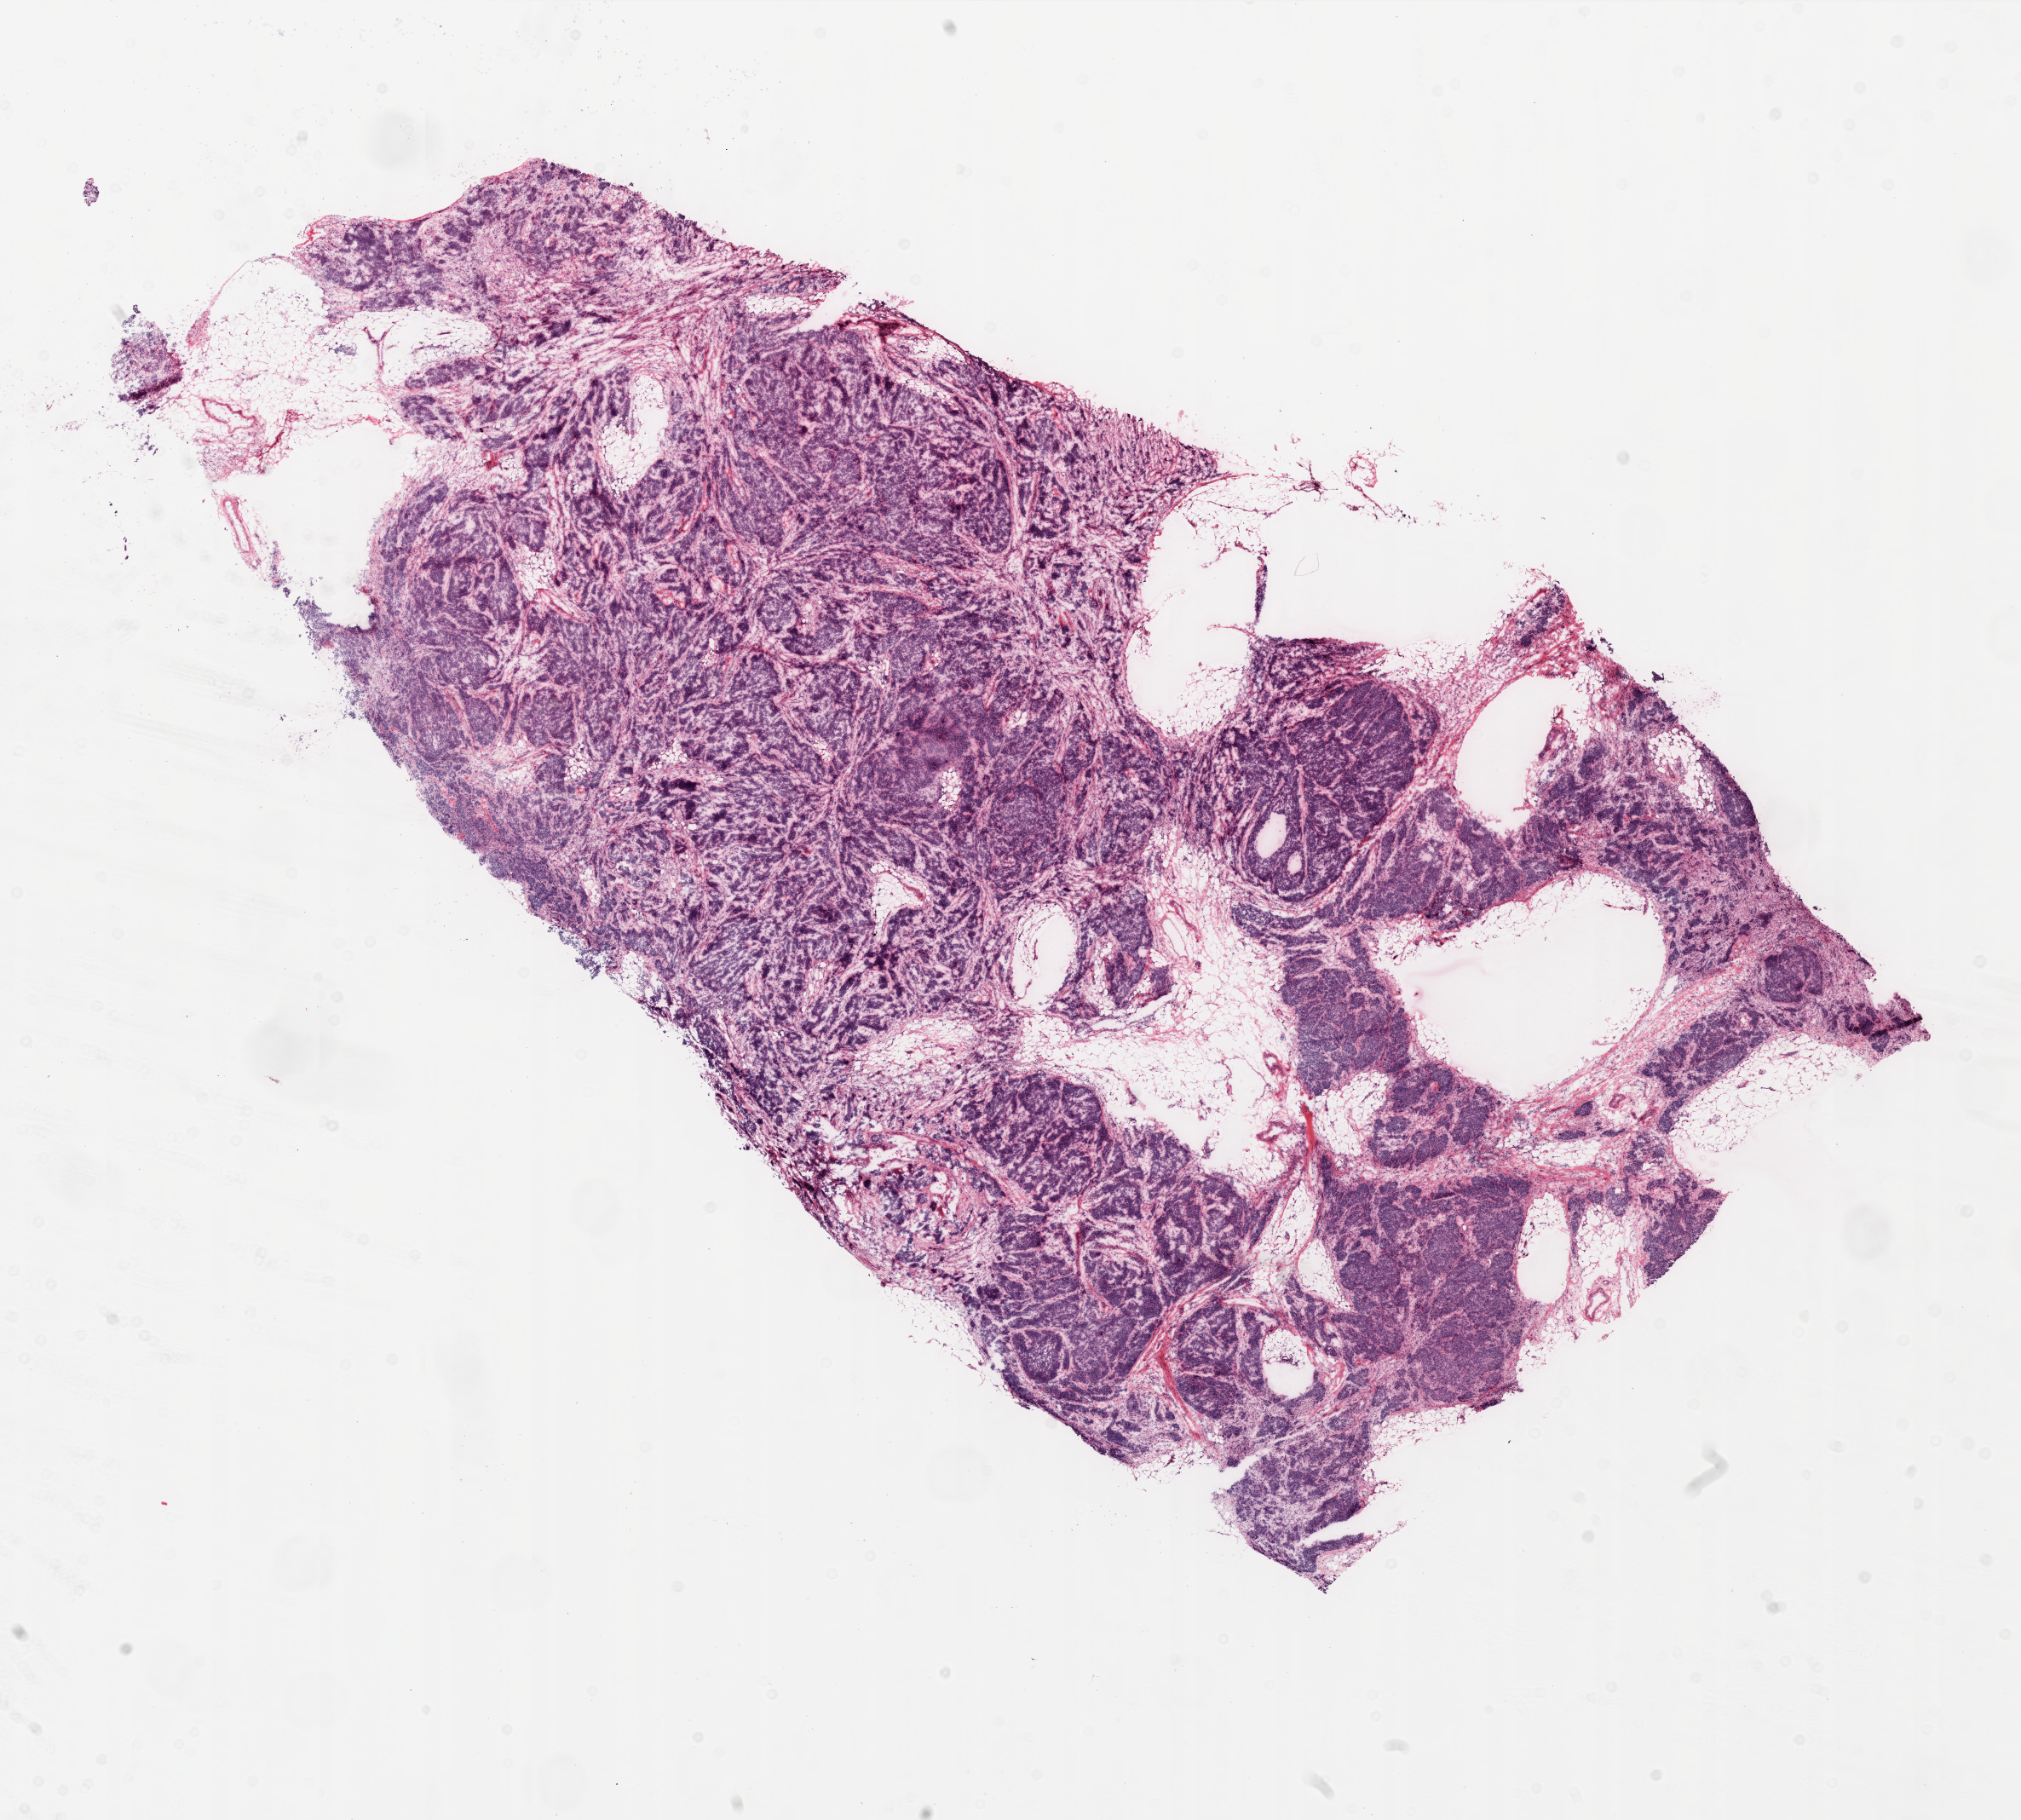
Whole-slide histology image, Hematoxylin and eosin (H&E) stained — a low-resolution overview of the entire scanned area, about 19.0 x 17.1 mm (slide scanned at 20x). Pathologist review of this section (percent, as recorded): tumour cells 85%, tumour nuclei 90%, stromal cells 15%, necrosis 0%.
Specimen: frozen section from the top of the tissue portion; primary tumour sample from the ovary.